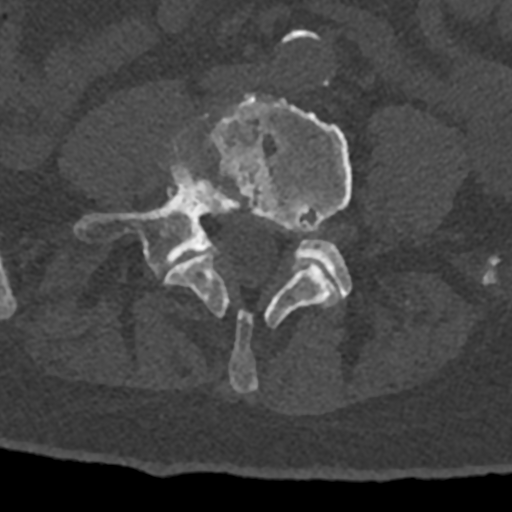
CT including the spine, one axial slice. Position 233 of 797 along the scan axis. Bone window (W 1800 / L 400 HU). 0.5 mm slice thickness. 512 × 512 image matrix, field of view 160 × 160 mm. Patient: male, 74 years. From the clinical record (not read from this slice): primary cancer: renal; vertebrae with lytic lesions (as recorded): T10, L1, L2, L3, L4, L5.
Outlined on this slice (semi-automatically segmented with operator editing):
- L4 vertebra: bounding box [x1, y1, x2, y2] px = [164, 93, 353, 392]
- L5 vertebra: [74, 137, 352, 298]